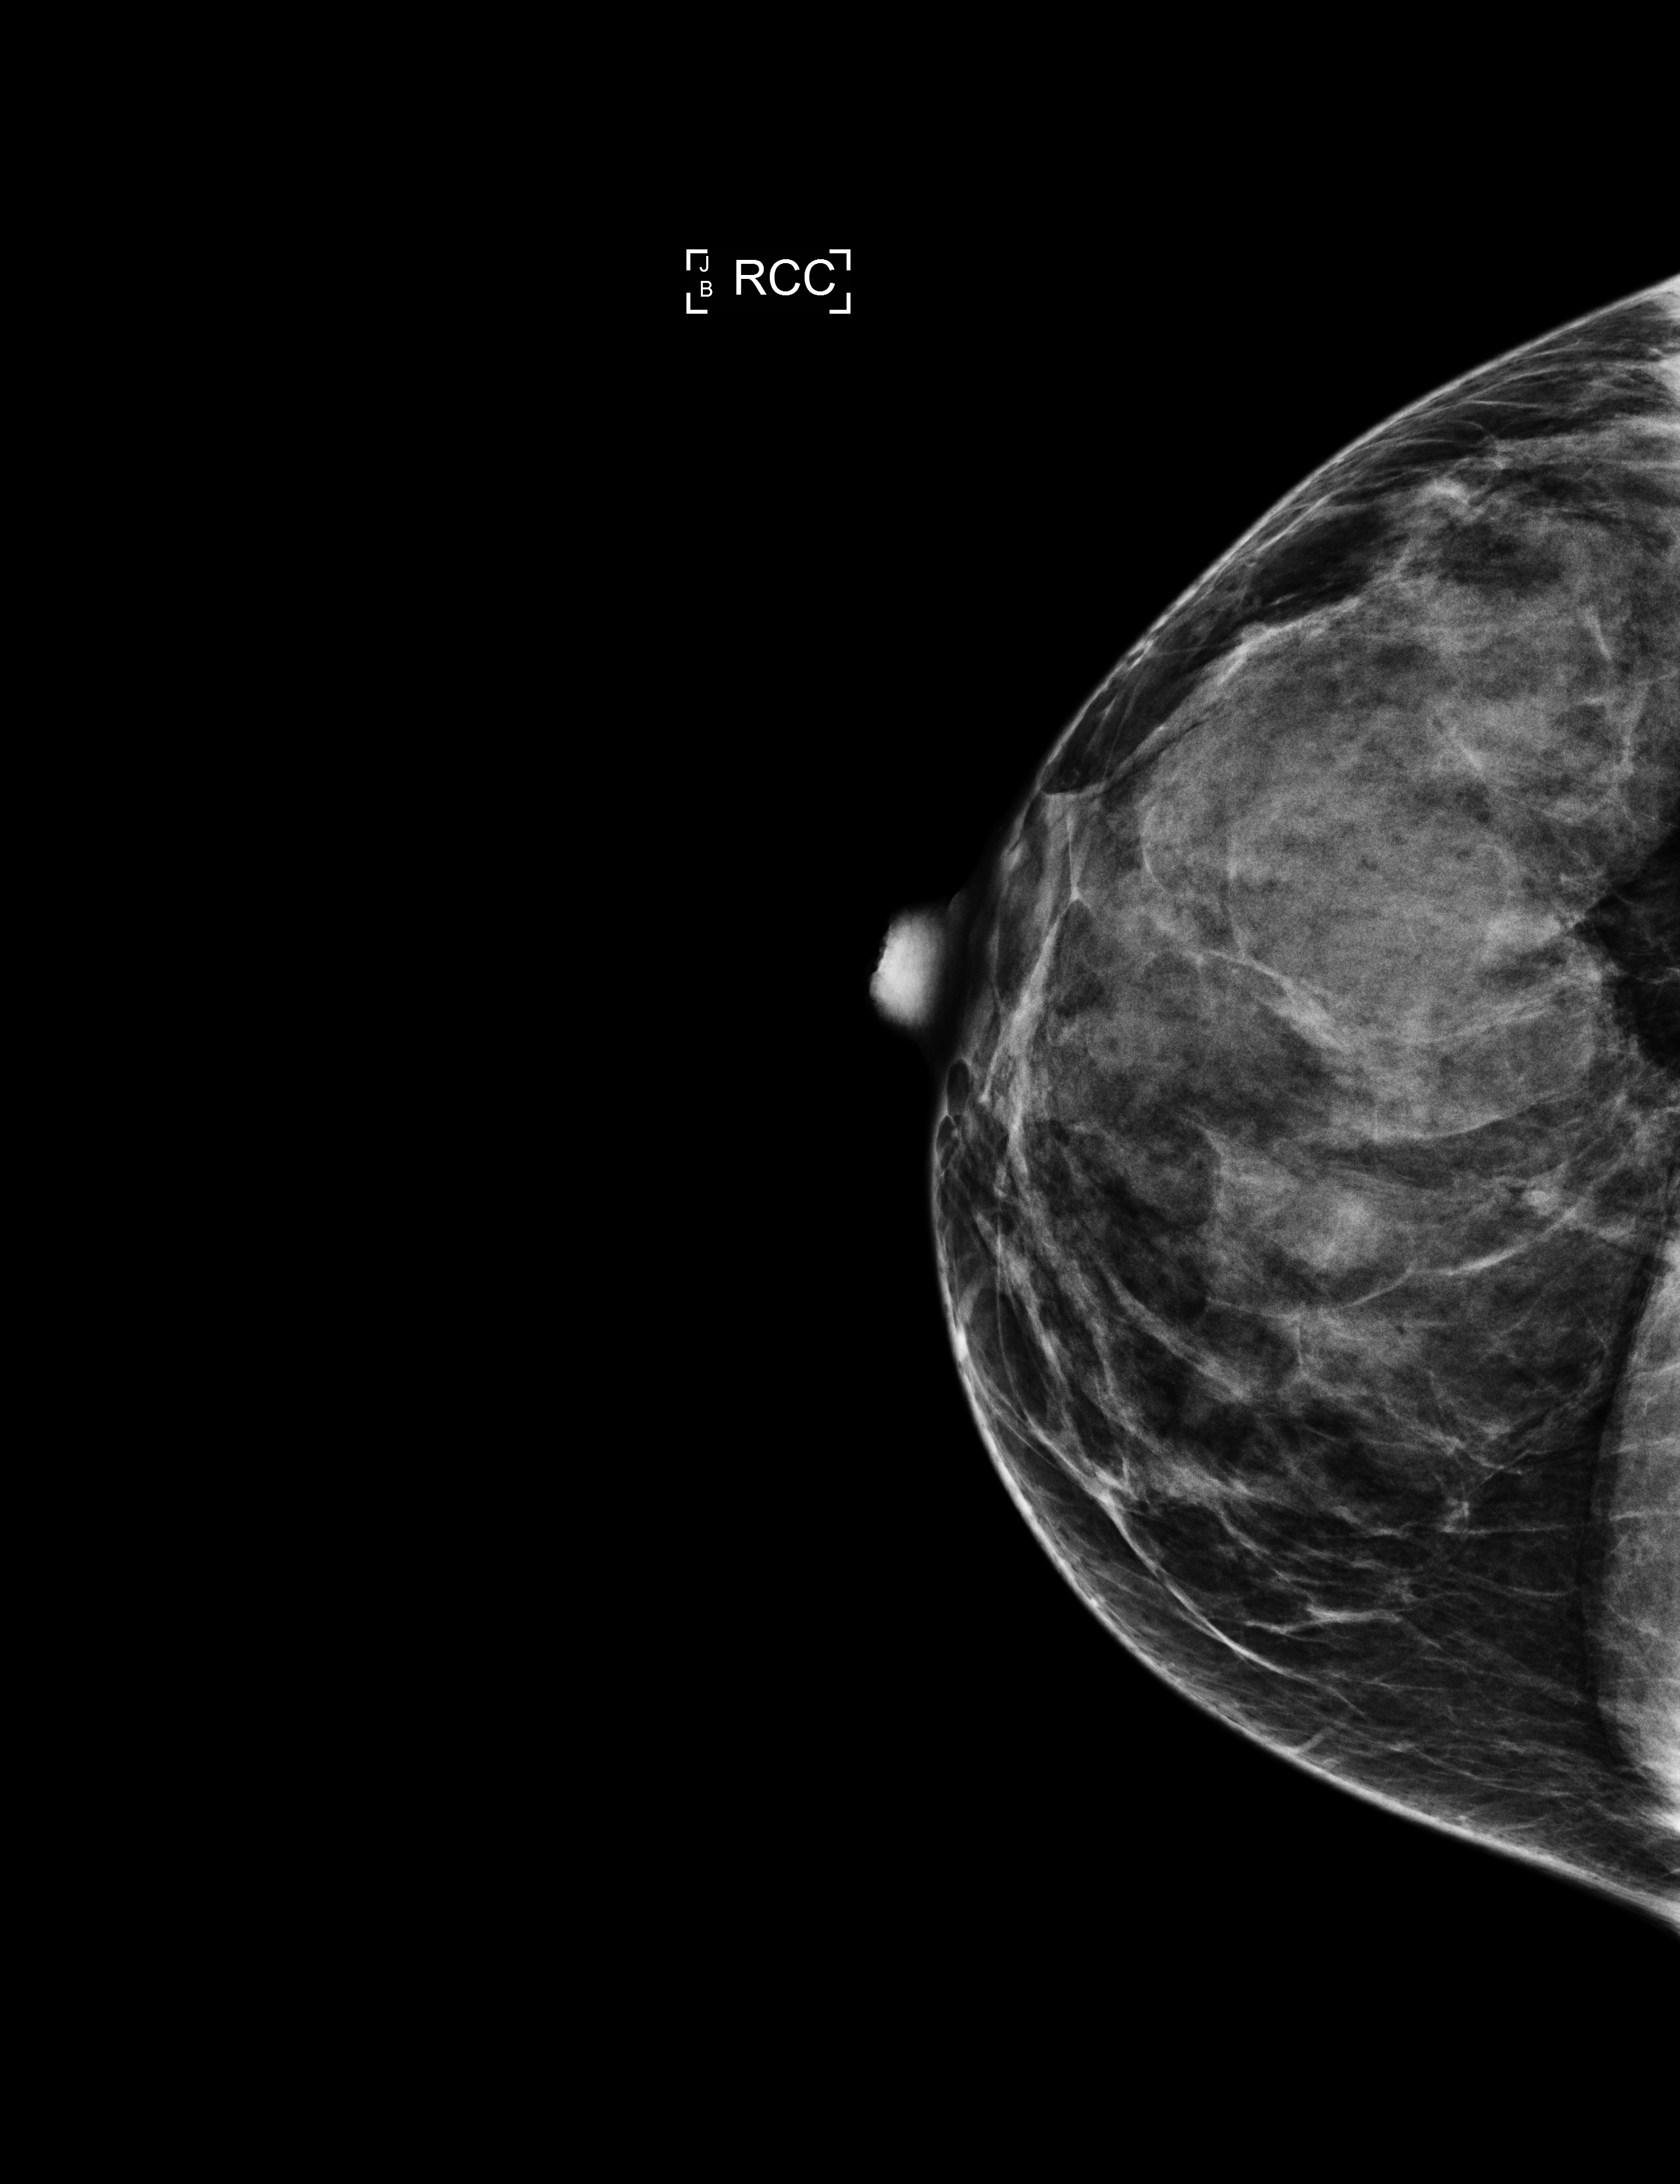
Annual screening mammography examination. Patient aged 47 years (female).
Image type: full-field digital mammogram. Breast: right. Projection: cranio-caudal projection.